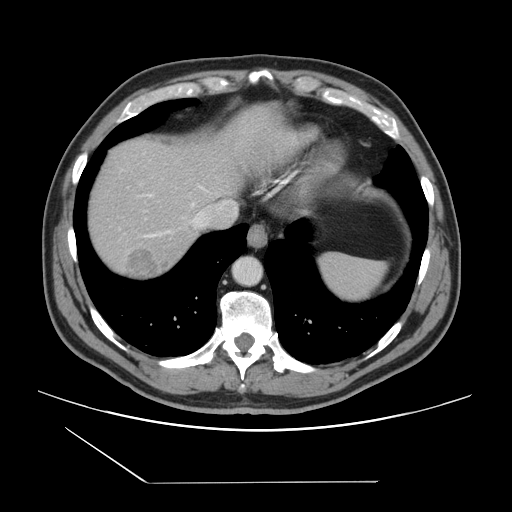
Contrast-enhanced abdominal CT, one axial slice. Slice 128 of 157 in the series (ordered by position). 120 kVp. Intravenous contrast given. Soft-tissue window (W 400 / L 40 HU). 2.5 mm slice thickness. 512 × 512 image matrix, field of view 407 × 407 mm. Male patient, age 61 years. Case-level facts recorded for this patient, not image findings: diagnosis: colorectal cancer liver metastases, imaged before liver resection.
Structures marked on this image (manually delineated by an expert):
- hepatic veins: bounding box (x1, y1, x2, y2) in pixels: (143, 194, 238, 238)
- liver: (87, 133, 243, 281)
- planned liver remnant (the part of the liver to remain after resection): (87, 137, 228, 231)
- liver metastasis: (125, 245, 174, 279)